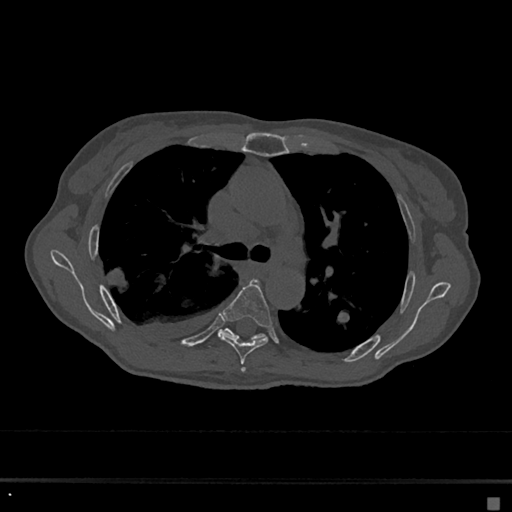
CT including the spine, one axial slice; slice 451 of 797 in the series (ordered by position); bone window (W 1800 / L 400 HU); 0.5 mm slice thickness; 512 × 512 image matrix, field of view 360 × 360 mm. Female patient, age 68 years. Case-level facts recorded for this patient, not image findings: primary cancer: renal.
Outlined on this slice (semi-automatically segmented with operator editing):
- T5 vertebra: bounding box [x1, y1, x2, y2] px = [220, 279, 272, 371]
- T6 vertebra: [218, 328, 266, 341]